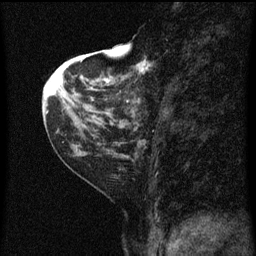
Breast MRI (dynamic contrast-enhanced), one sagittal slice; position 22 of 60 along the scan axis; dynamic contrast-enhanced series, image 2 of 3 at this slice position (ordered by acquisition); 1.5 T; TE 4.2 ms, TR 8 ms; 2 mm slice thickness; 256 × 256 image matrix, field of view 180 × 180 mm. Patient: female, 48 years.
Structures marked on this image (semi-automatically segmented with operator editing):
- analysis volume of interest (the breast-tissue region the enhancement analysis was run in; not a lesion): bounding box (x1, y1, x2, y2) in pixels: (128, 54, 175, 125)
- tumour enhancement mask (voxels above the 70 % enhancement threshold inside the analysis volume of interest): (130, 60, 152, 125)